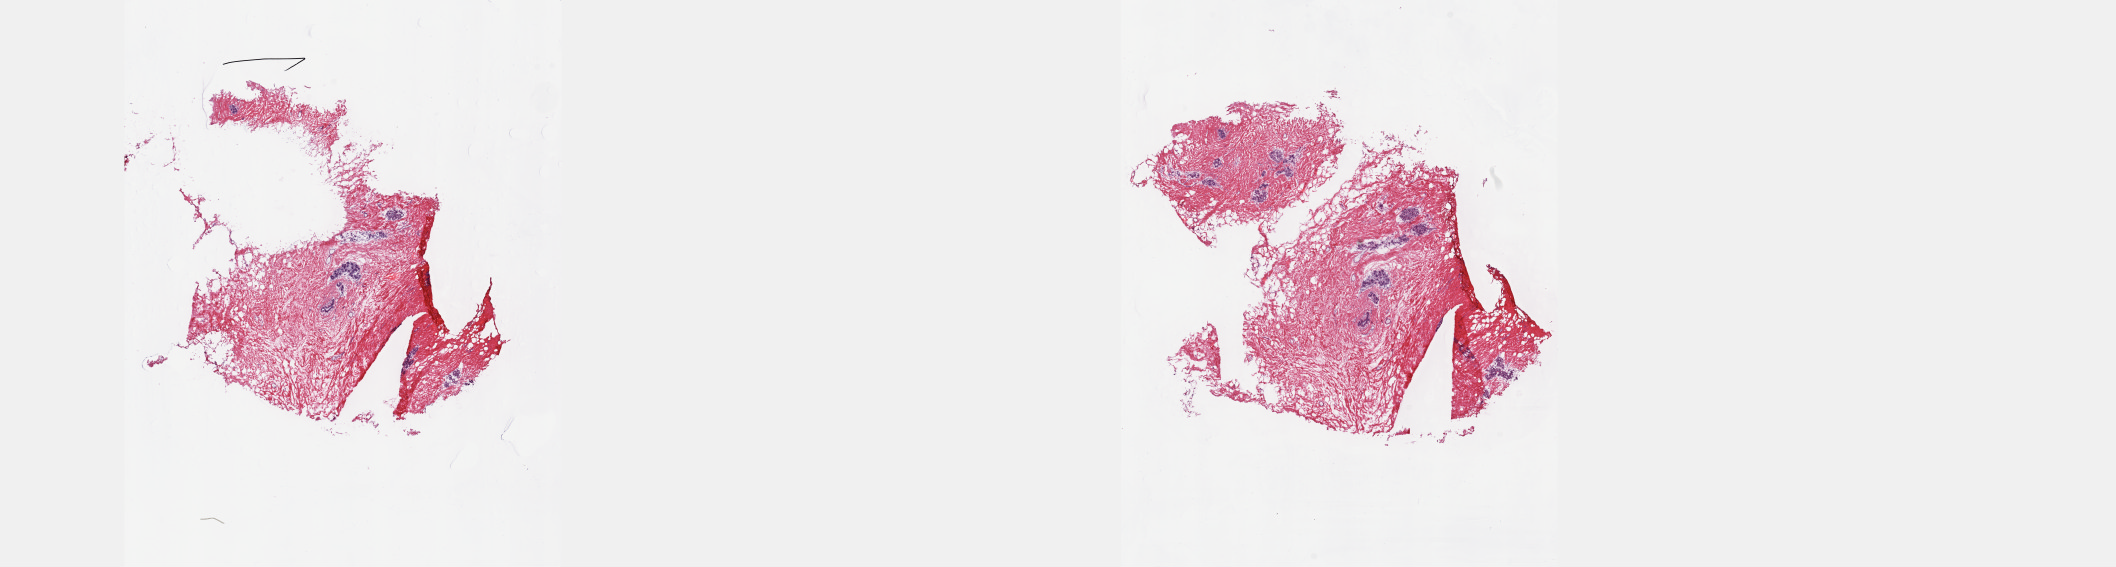
H&E whole-slide image — whole scanned area (about 34.1 x 9.1 mm) shown as a low-resolution overview; frozen section from the top of the tissue portion; sample: solid tissue normal (non-tumour tissue), breast. Patient: female, age at initial diagnosis 46 years. Pathologist review of this section (percent, as recorded): tumour cells 0%, tumour nuclei 0%, normal cells 100%, stromal cells 0%, necrosis 0%. Inflammatory infiltration, as recorded: lymphocyte infiltration 1%, monocyte infiltration 0%, neutrophil infiltration 0%.
- this section: solid tissue normal (non-tumour) sample from the same patient
- patient diagnosis: Lobular carcinoma, NOS